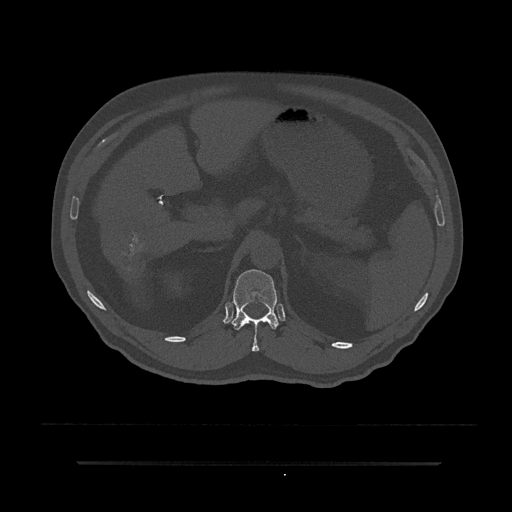
CT including the spine, one axial slice; slice 215 of 797 in the series (ordered by position); bone window (W 1800 / L 400 HU); 0.5 mm slice thickness; 512 × 512 image matrix, field of view 464 × 464 mm. Male patient, age 59 years. From the clinical record (not read from this slice): primary cancer: bile ducts; vertebrae with lytic lesions (as recorded): T10.
Outlined on this slice (semi-automatically segmented with operator editing):
- T12 vertebra: bounding box [x1, y1, x2, y2] px = [232, 269, 279, 352]